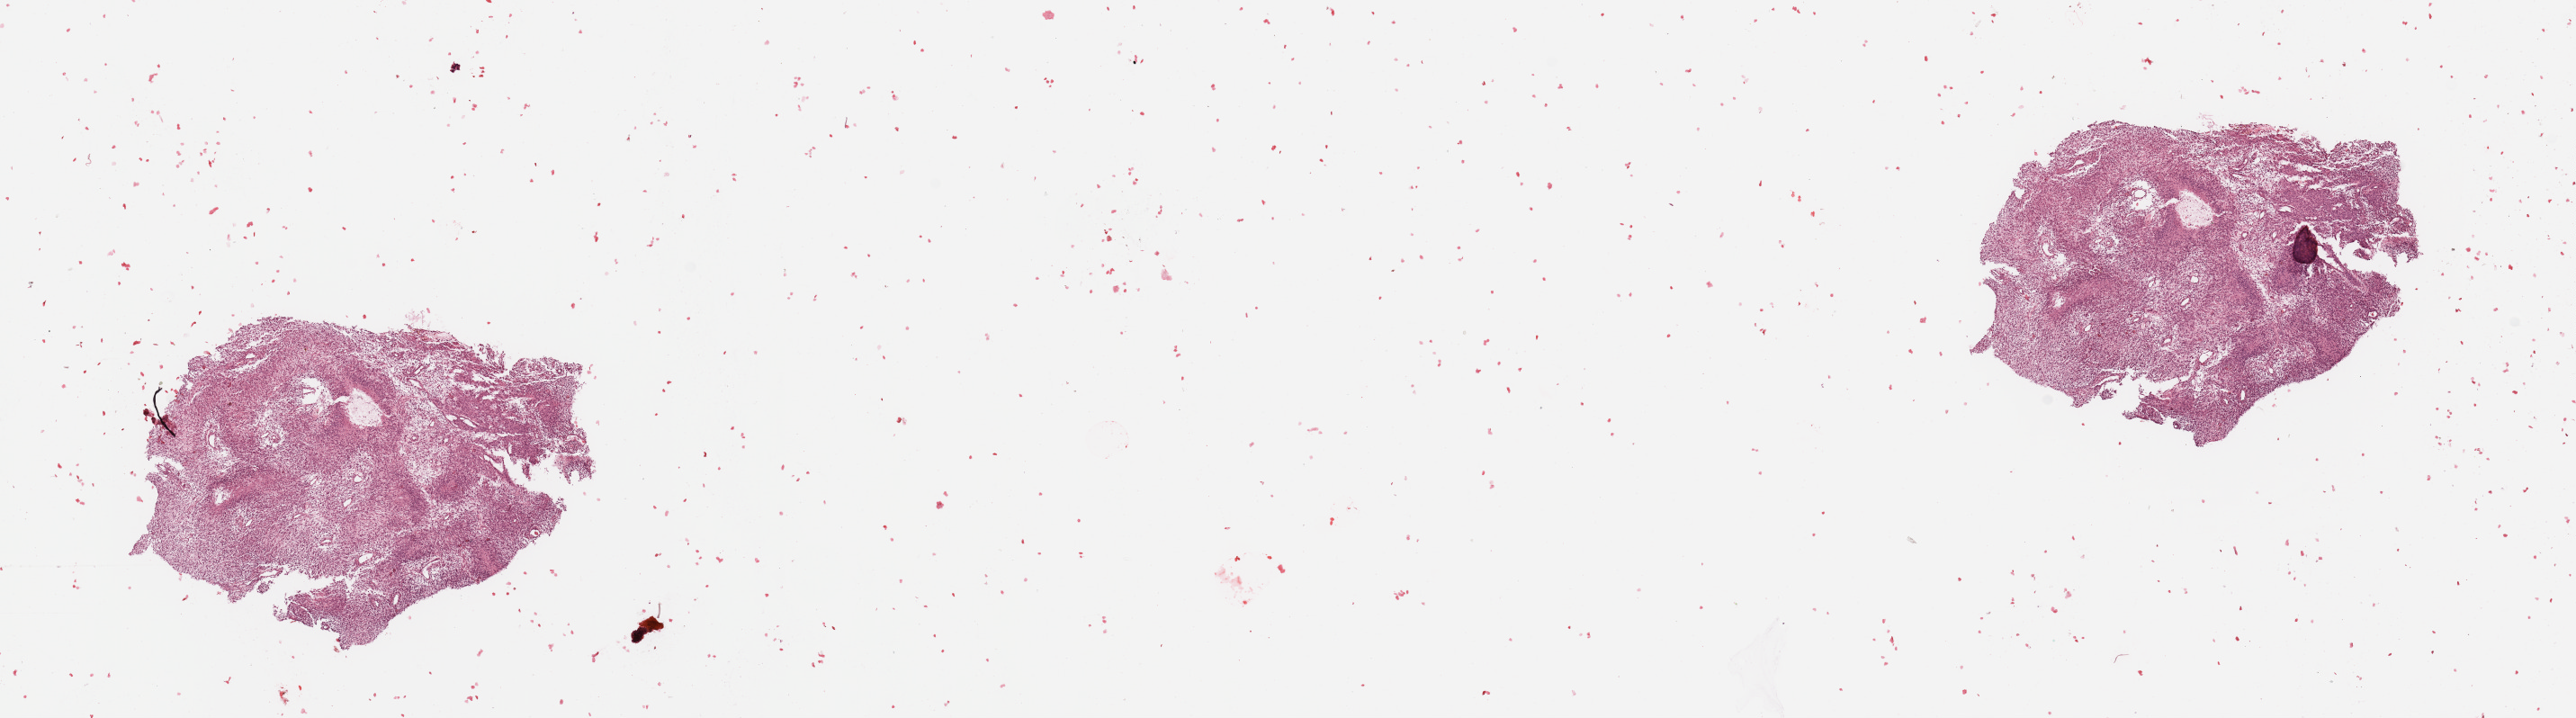
Digitized H&E-stained tissue section (whole slide), low-resolution overview of the scanned area, about 22.6 x 6.3 mm. Brain, tumour tissue. 63-year-old male patient.
Histologic diagnosis: Glioblastoma.